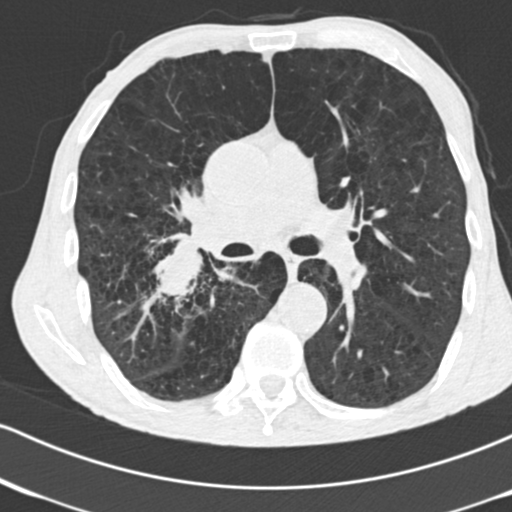
Low-dose screening chest CT, one axial slice. Position 98 of 182 along the scan axis. Reconstruction kernel B30f. 120 kVp. Lung window (W 1500 / L -600 HU). 2 mm slice thickness. 512 × 512 image matrix, field of view 316 × 316 mm.
Structures marked on this image (expert manual segmentation):
- lesion 1 (tumor, lower lobe of right lung): bounding box (x1, y1, x2, y2) in pixels: (155, 242, 204, 294)